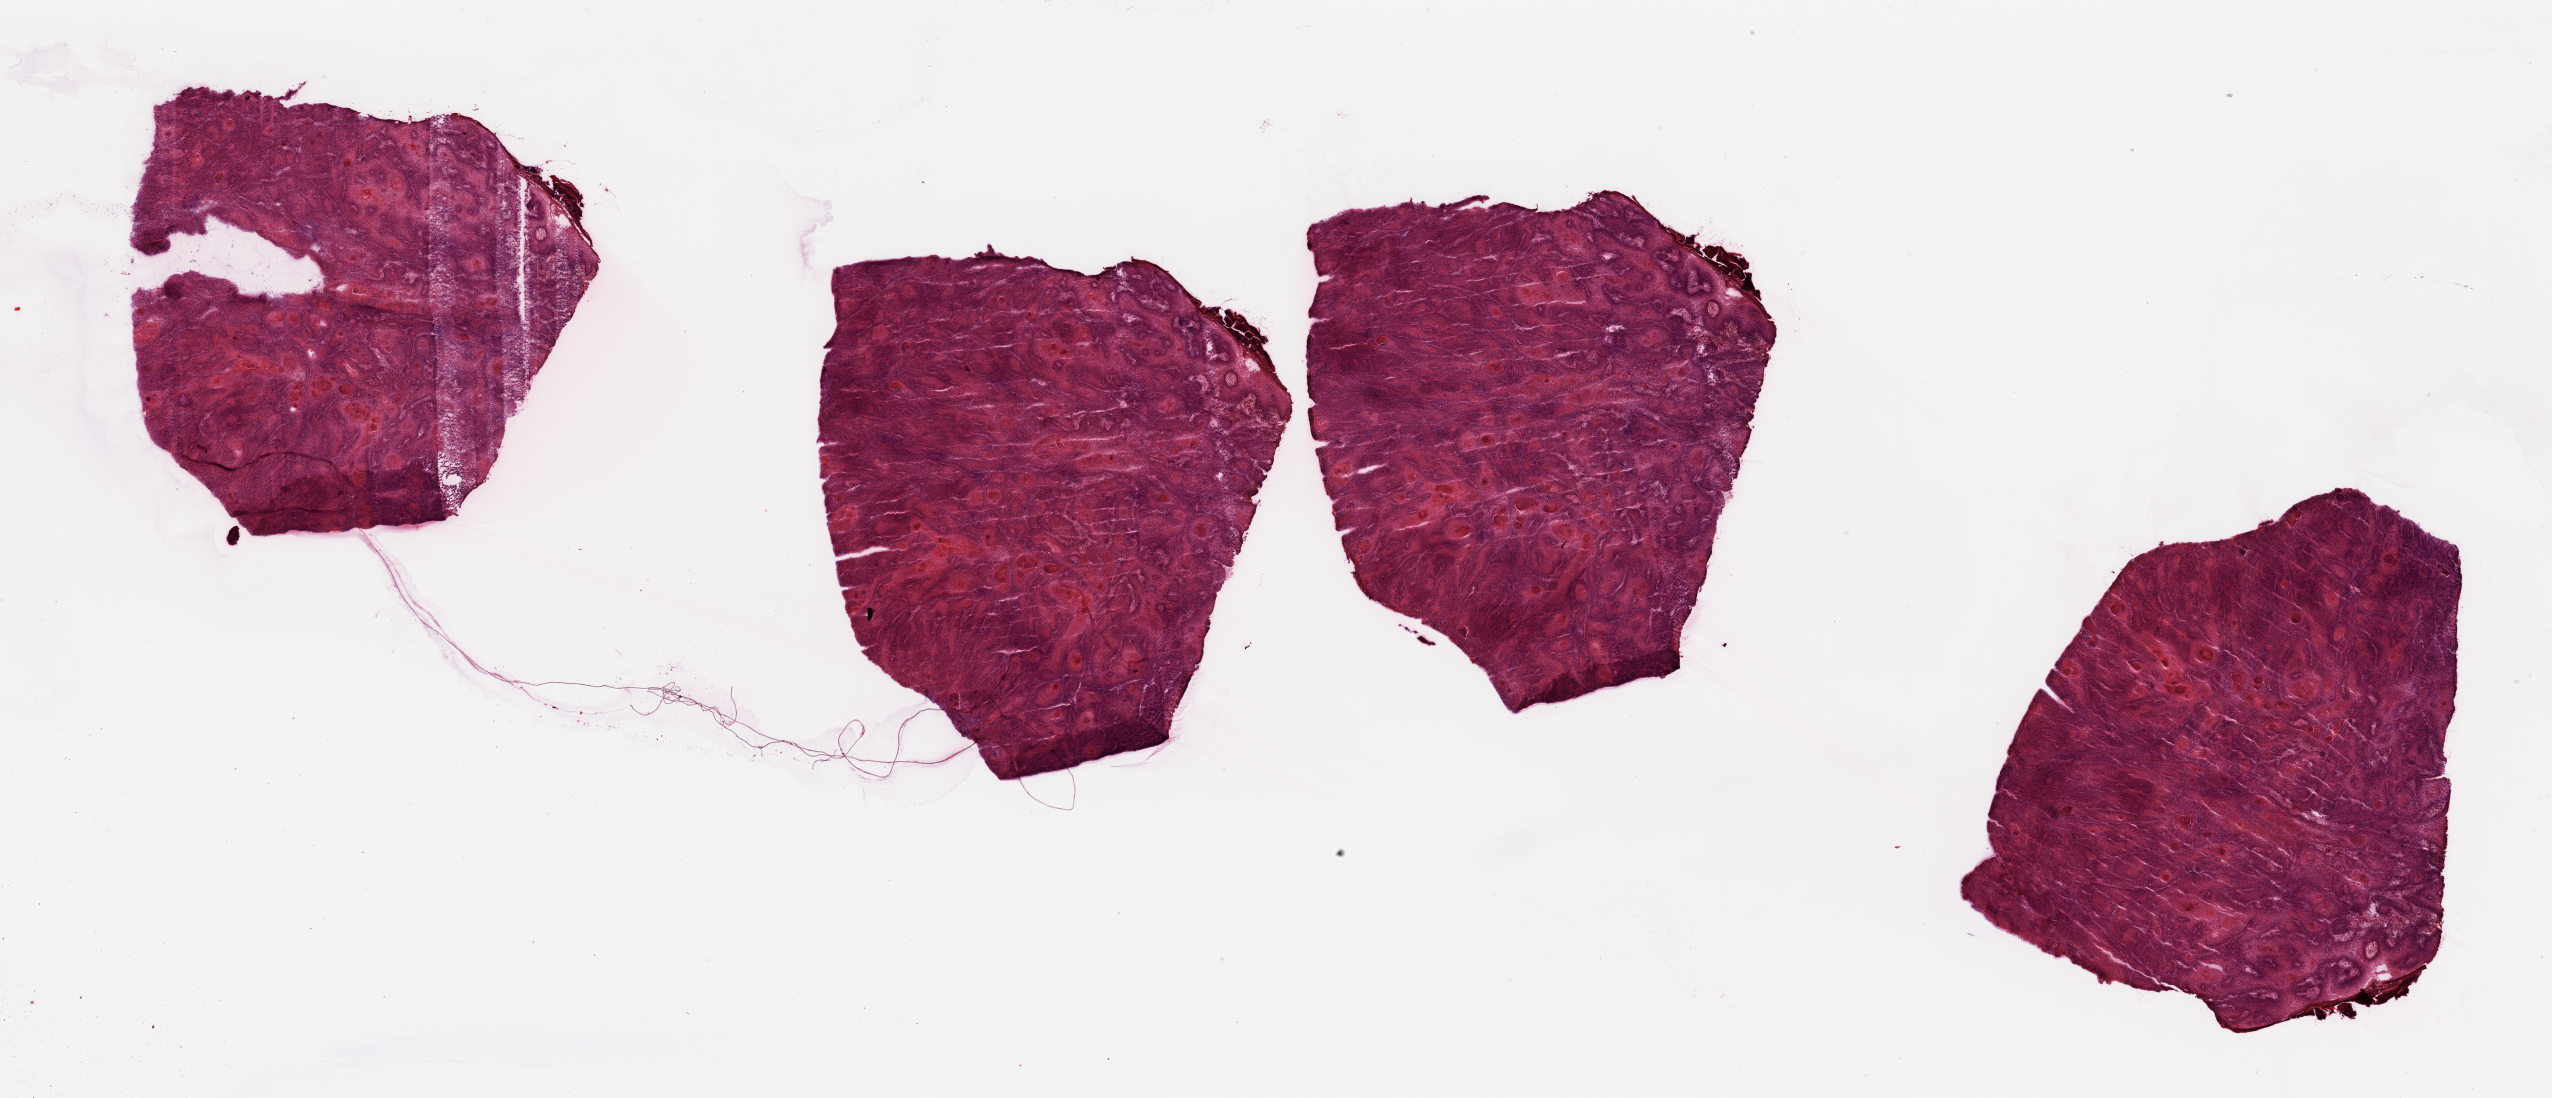
Whole-slide histology image, H&E-stained — shown as a low-resolution overview of the whole scanned area (about 40.4 x 17.4 mm, slide scanned at 20x), tumour tissue sample, sampled site: lip. Male, 54 y/o. Histologic grade: G2 (moderately differentiated). Slide review estimates, as recorded: tumour nuclei 85%, necrosis 10%.
Diagnosis: Squamous cell carcinoma, NOS (lip, NOS). AJCC pathologic stage: II. Primary tumour site (as recorded): lip.